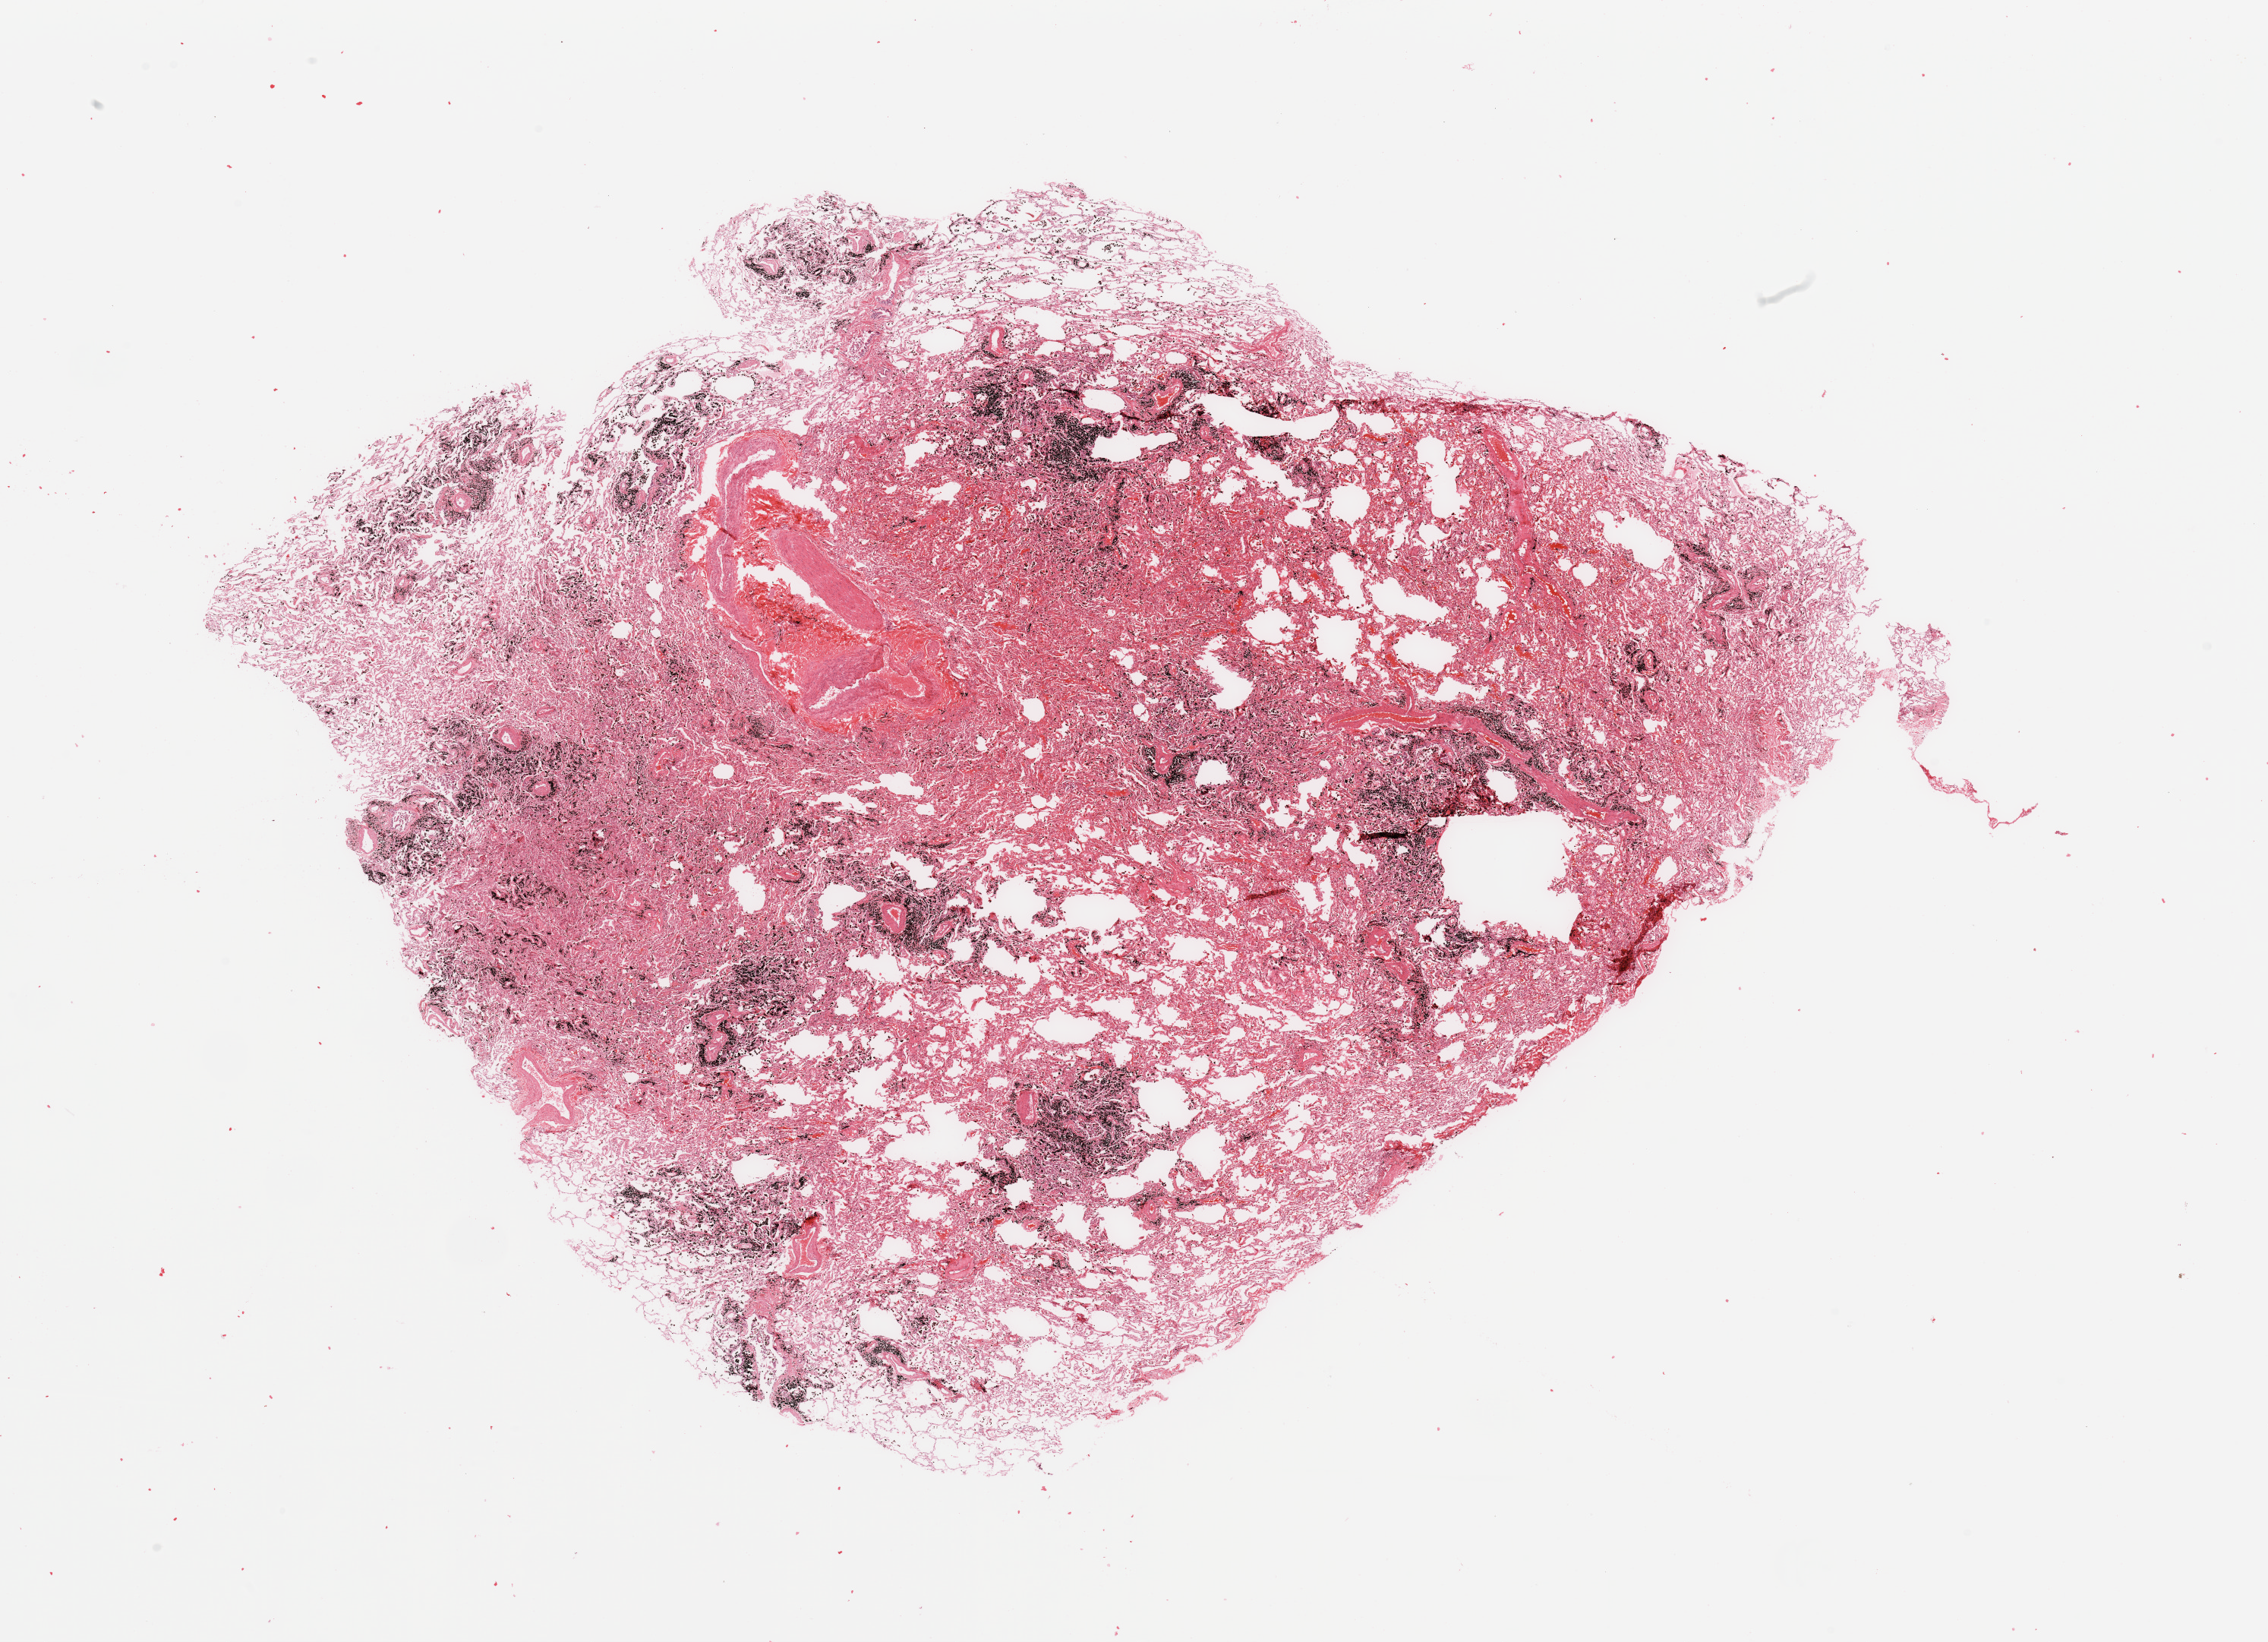
Digitized H&E-stained tissue section (whole slide) — a low-resolution overview of the entire scanned area, about 23.6 x 17.1 mm (slide scanned at 20x). Normal (non-tumour) tissue sample, sampled site: lung. Patient: male, age 56 years.
This section: normal (non-tumour) tissue from the same patient. Patient diagnosis: Adenocarcinoma, NOS.